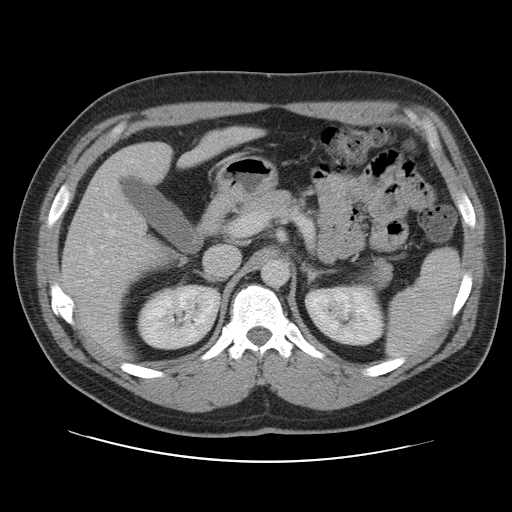
Contrast-enhanced abdominal CT, one axial slice. Slice 64 of 109 in the series (ordered by position). 120 kVp. Intravenous contrast given. Soft-tissue window (W 400 / L 40 HU). 5 mm slice thickness. 512 × 512 image matrix. Male patient, age 35 years. From the clinical record (not read from this slice): diagnosis: colorectal cancer liver metastases, imaged before liver resection; multiple liver metastases: yes; largest metastasis: 2.8 cm; disease in both lobes: yes.
Annotated regions visible in this slice (outlined manually by an expert reader):
- liver: box from (x=62, y=128) to (x=255, y=354) px
- planned liver remnant (the part of the liver to remain after resection): (x=62, y=128)–(x=256, y=355)
- portal vein (with intrahepatic branches): (x=81, y=212)–(x=140, y=285)